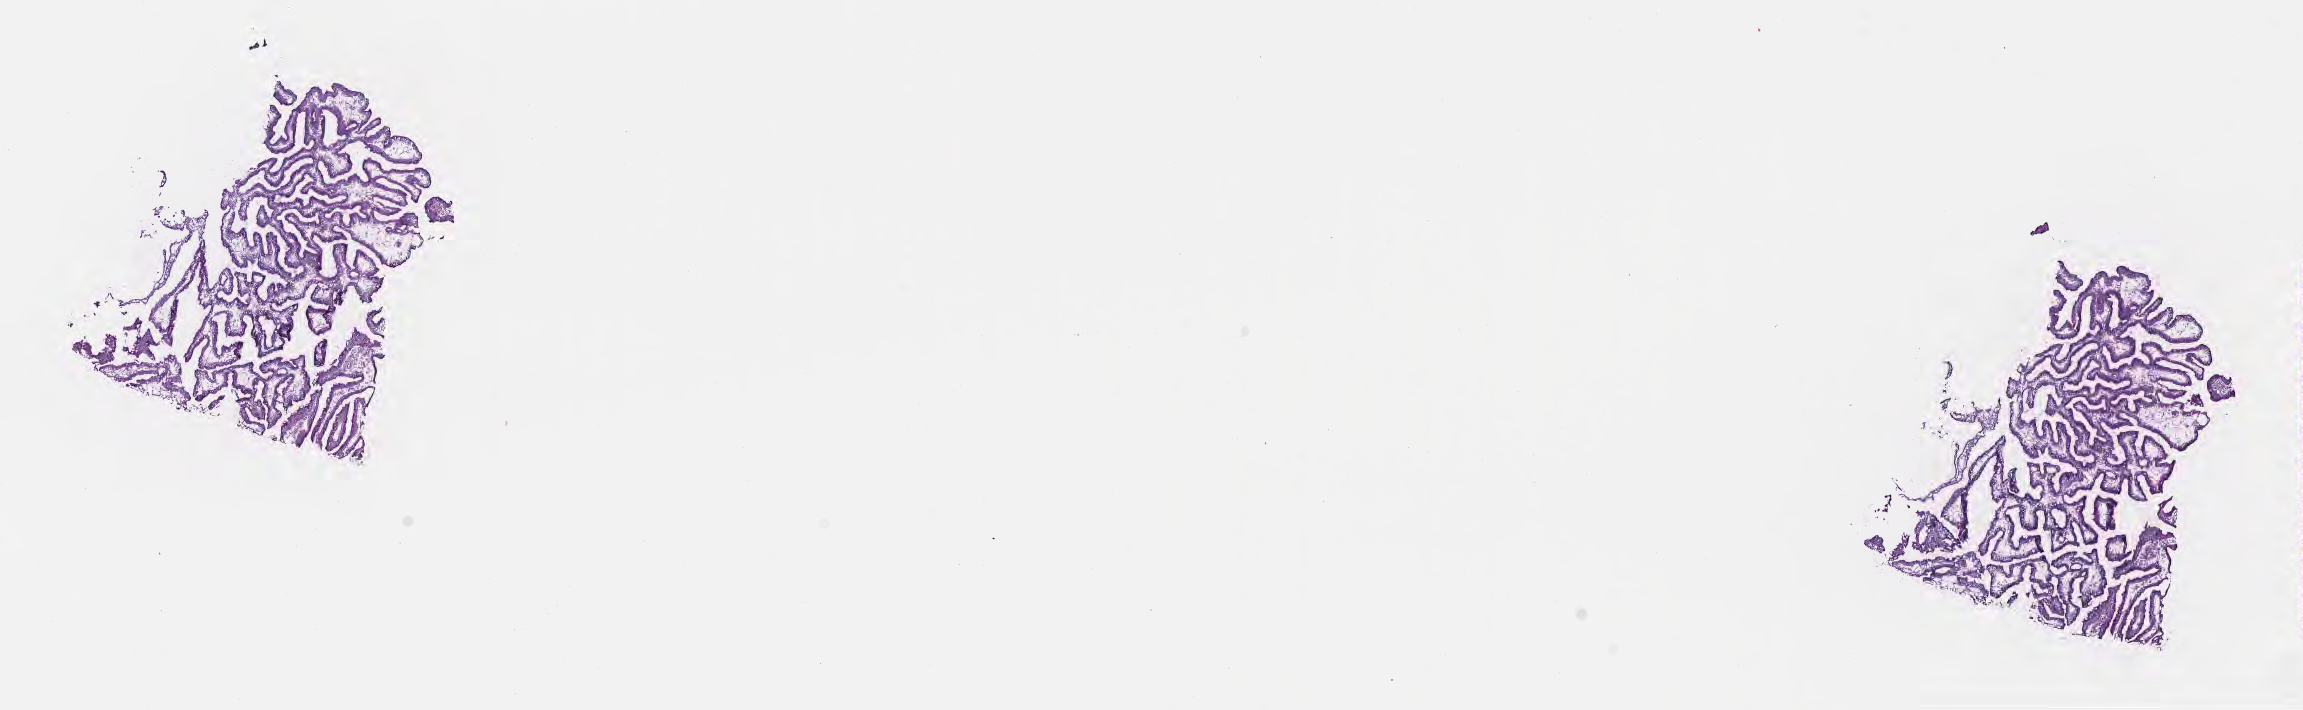
Digitized H&E-stained section, a low-resolution overview of the entire scanned area, about 18.6 x 5.7 mm. Frozen section. Specimen: primary tumor. Site: duodenum. Patient: female, age at initial diagnosis 59 years. Pathologist review of this section (percent, as recorded): tumor cells 85%, tumor nuclei 85%, stromal cells 15%, necrosis 0%, normal cells 0%. Inflammatory infiltration, as recorded: lymphocyte infiltration 5%, monocyte infiltration 2%, neutrophil infiltration 4%.
Section: top of the tissue portion. Histologic diagnosis: Tubulovillous adenoma, NOS. AJCC pathologic stage: Stage I.